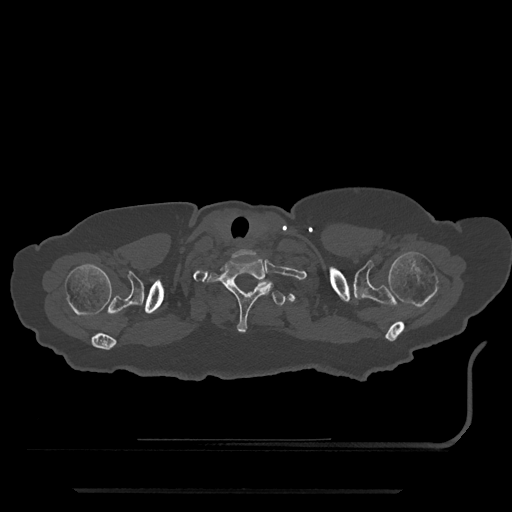
CT including the spine, one axial slice. Position 706 of 797 along the scan axis. Reconstruction kernel Br40s/3. 120 kVp. Bone window (W 1800 / L 400 HU). 0.5 mm slice thickness. 512 × 512 image matrix, field of view 440 × 440 mm. Patient: female, 51 years. Case-level facts recorded for this patient, not image findings: primary cancer: neuro; vertebrae with lytic lesions (as recorded): T8.
Outlined on this slice (semi-automatically segmented with operator editing):
- T1 vertebra: bounding box (x1, y1, x2, y2) in pixels: (208, 259, 274, 333)
- T2 vertebra: (256, 280, 285, 307)